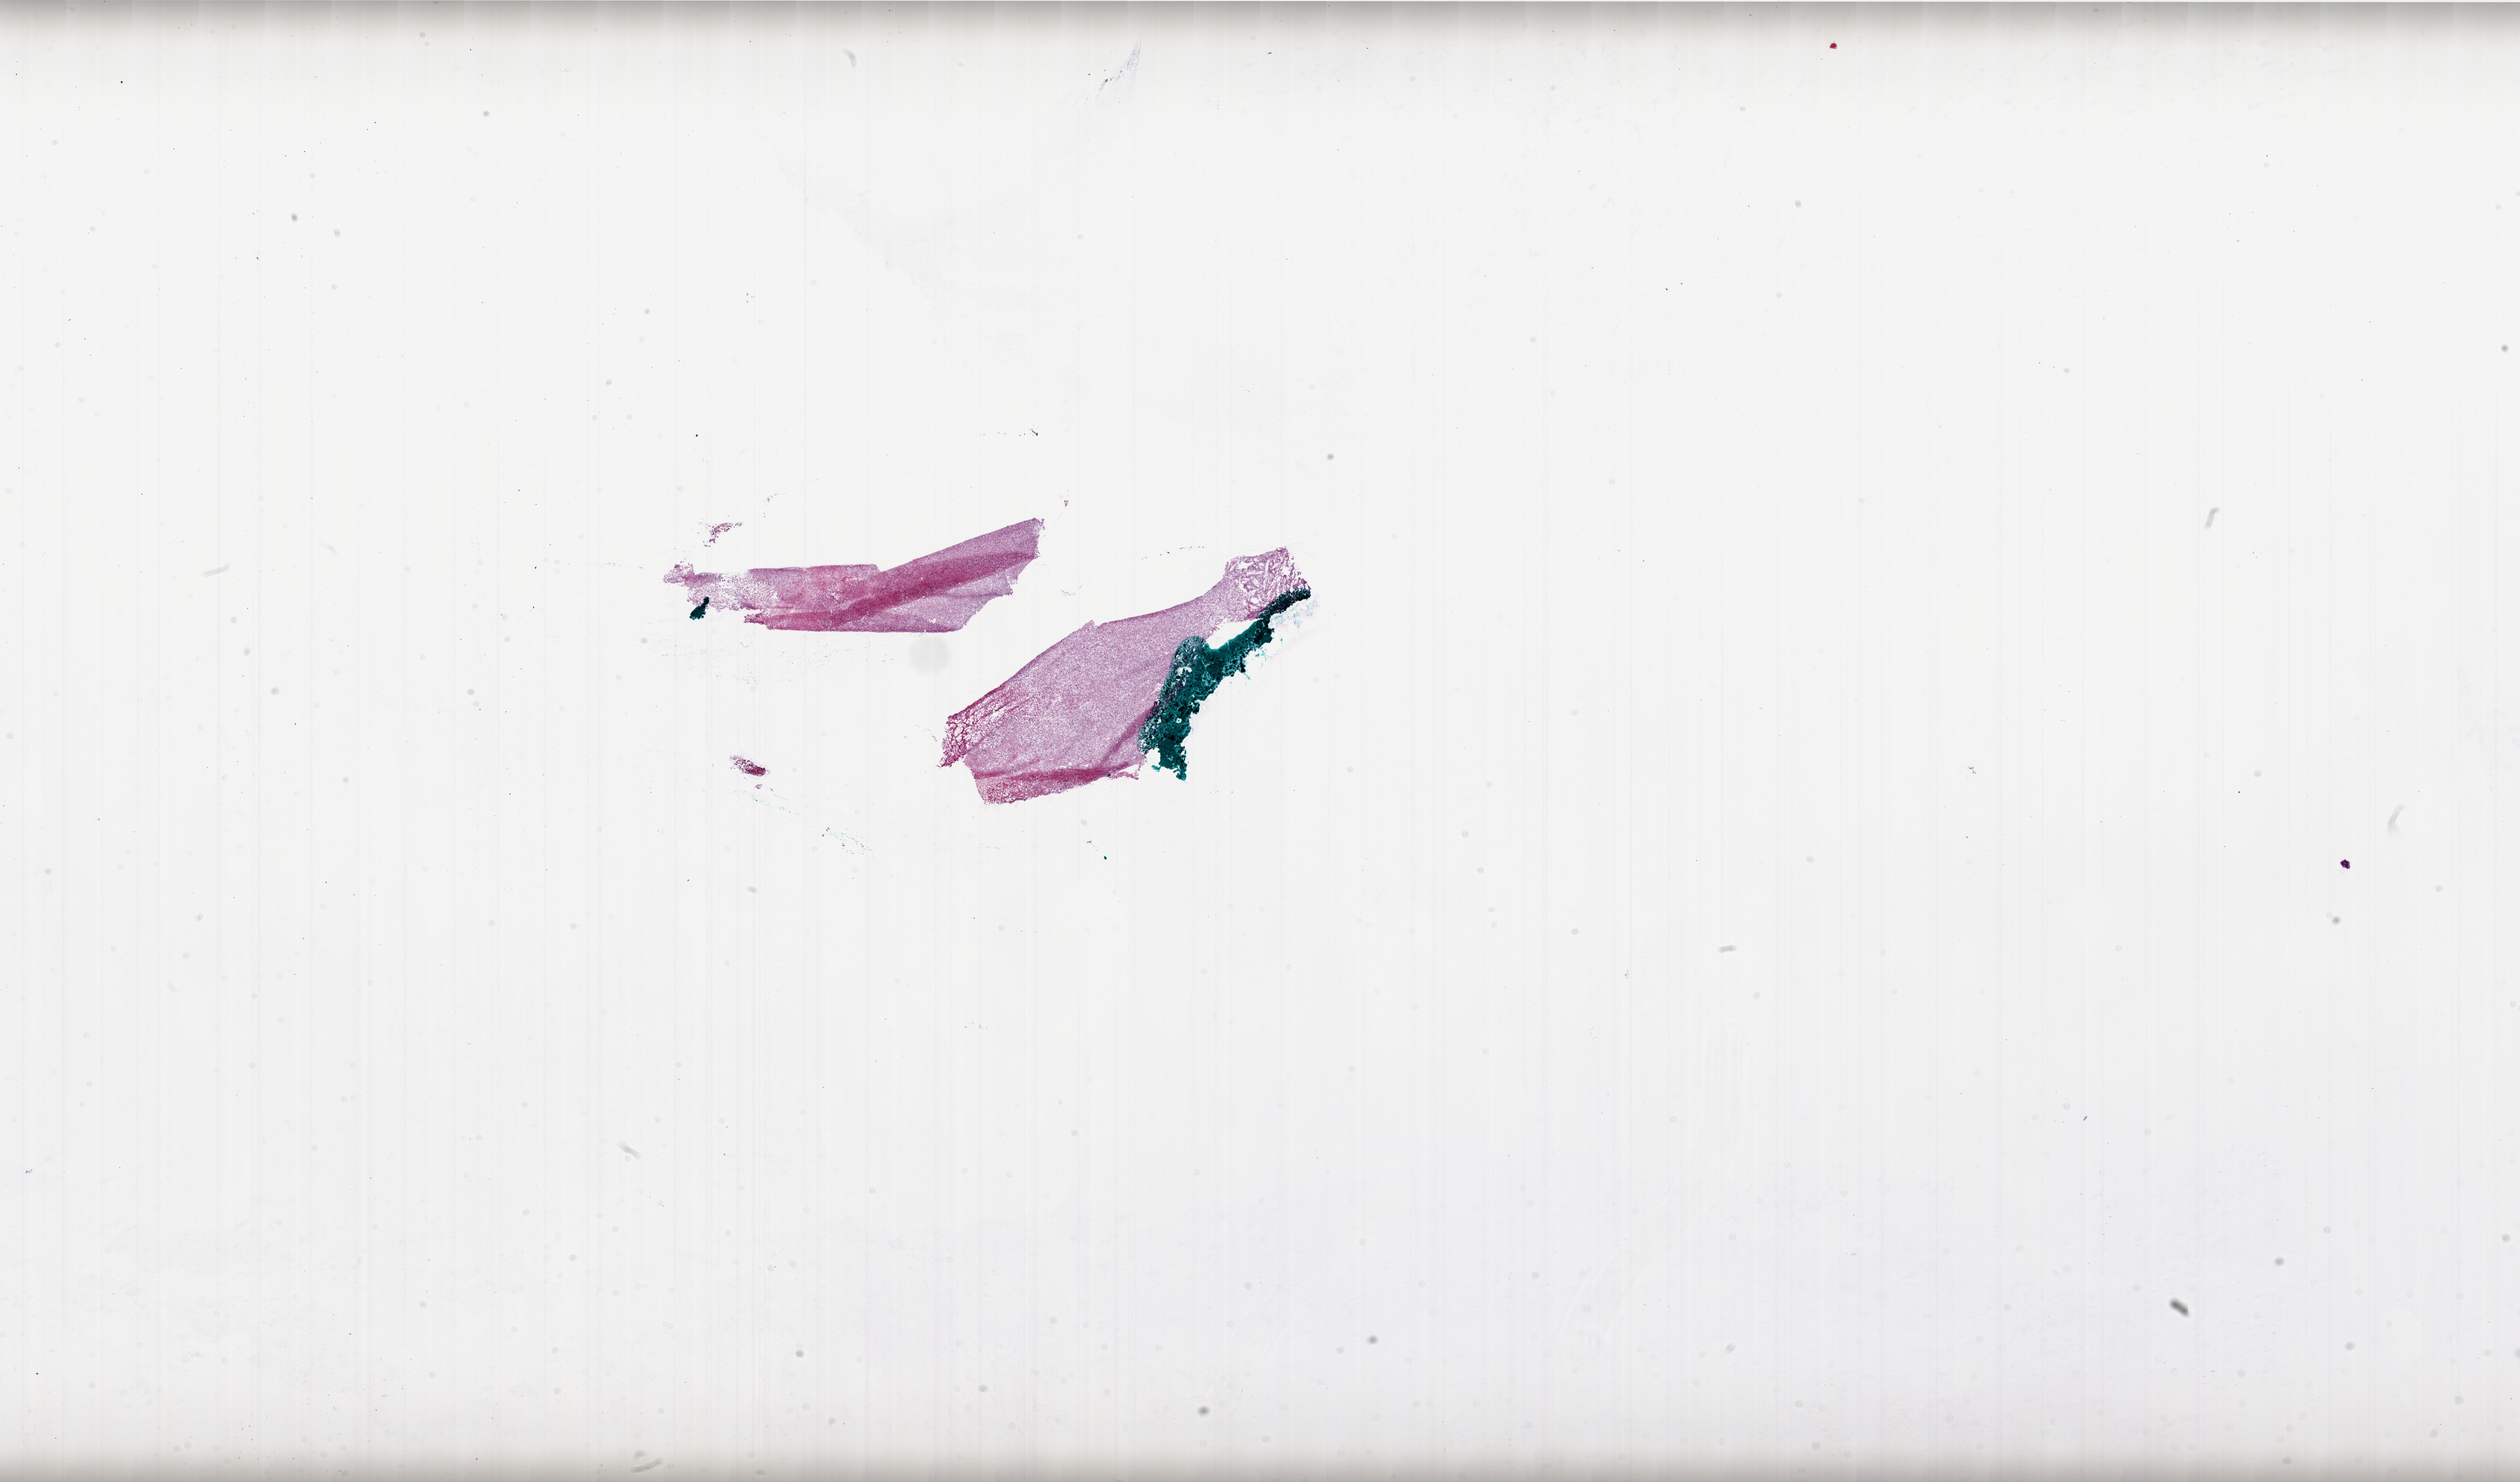
H&E whole-slide image, low-resolution overview of the scanned area, about 38.0 x 22.3 mm (from a 20x scan), frozen section from the bottom of the tissue portion, brain, primary tumour sample. Male, age 71 years at initial diagnosis. Pathologist review of this section (percent, as recorded): tumour cells 95%, tumour nuclei 100%, normal cells 0%, stromal cells 0%, necrosis 5%.
* histologic diagnosis: Glioblastoma